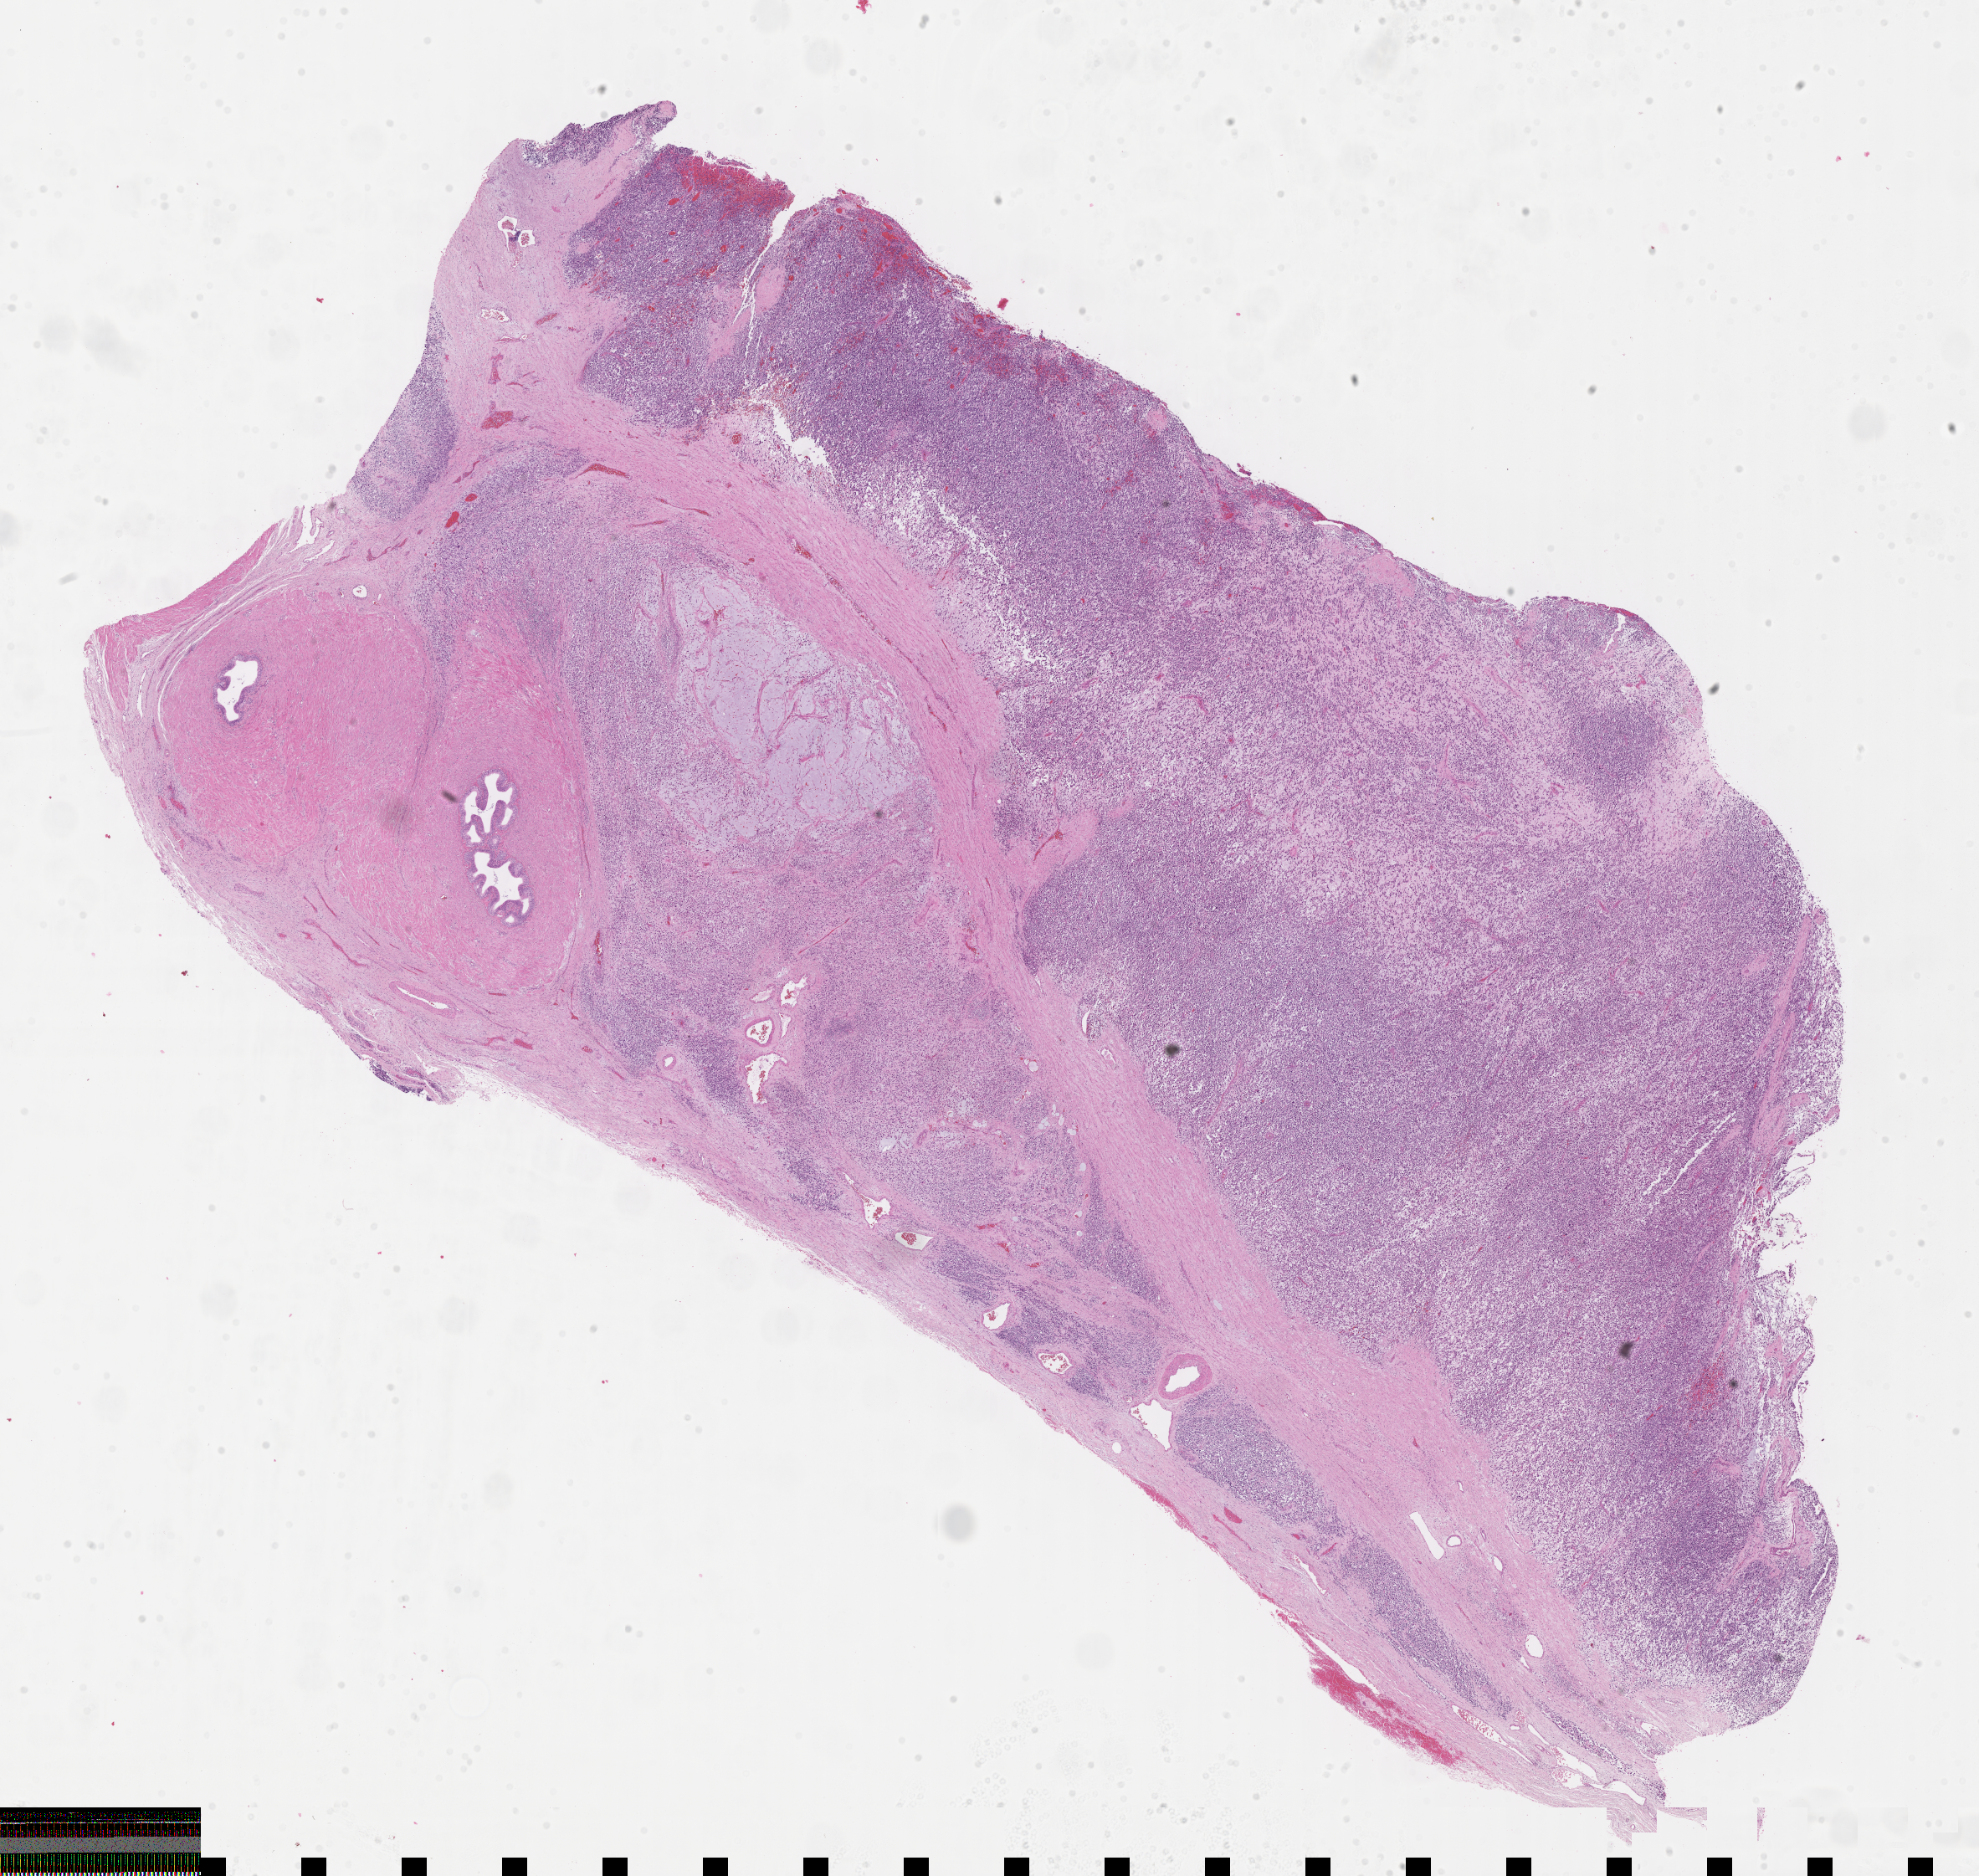
Whole-slide image, H&E stain of tumor tissue, shown as a low-resolution overview of the whole scanned area (about 19.1 x 18.1 mm); FFPE section; site: testicle, left. Male patient, age at diagnosis 17.8 years.
Stage (as recorded): 1. Primary site (case record): testis-Paratestis. Diagnosis: rhabdomyosarcoma; histological classification: embryonal rhabdomyosarcoma. Metastatic status at presentation (as recorded): non-metastatic.